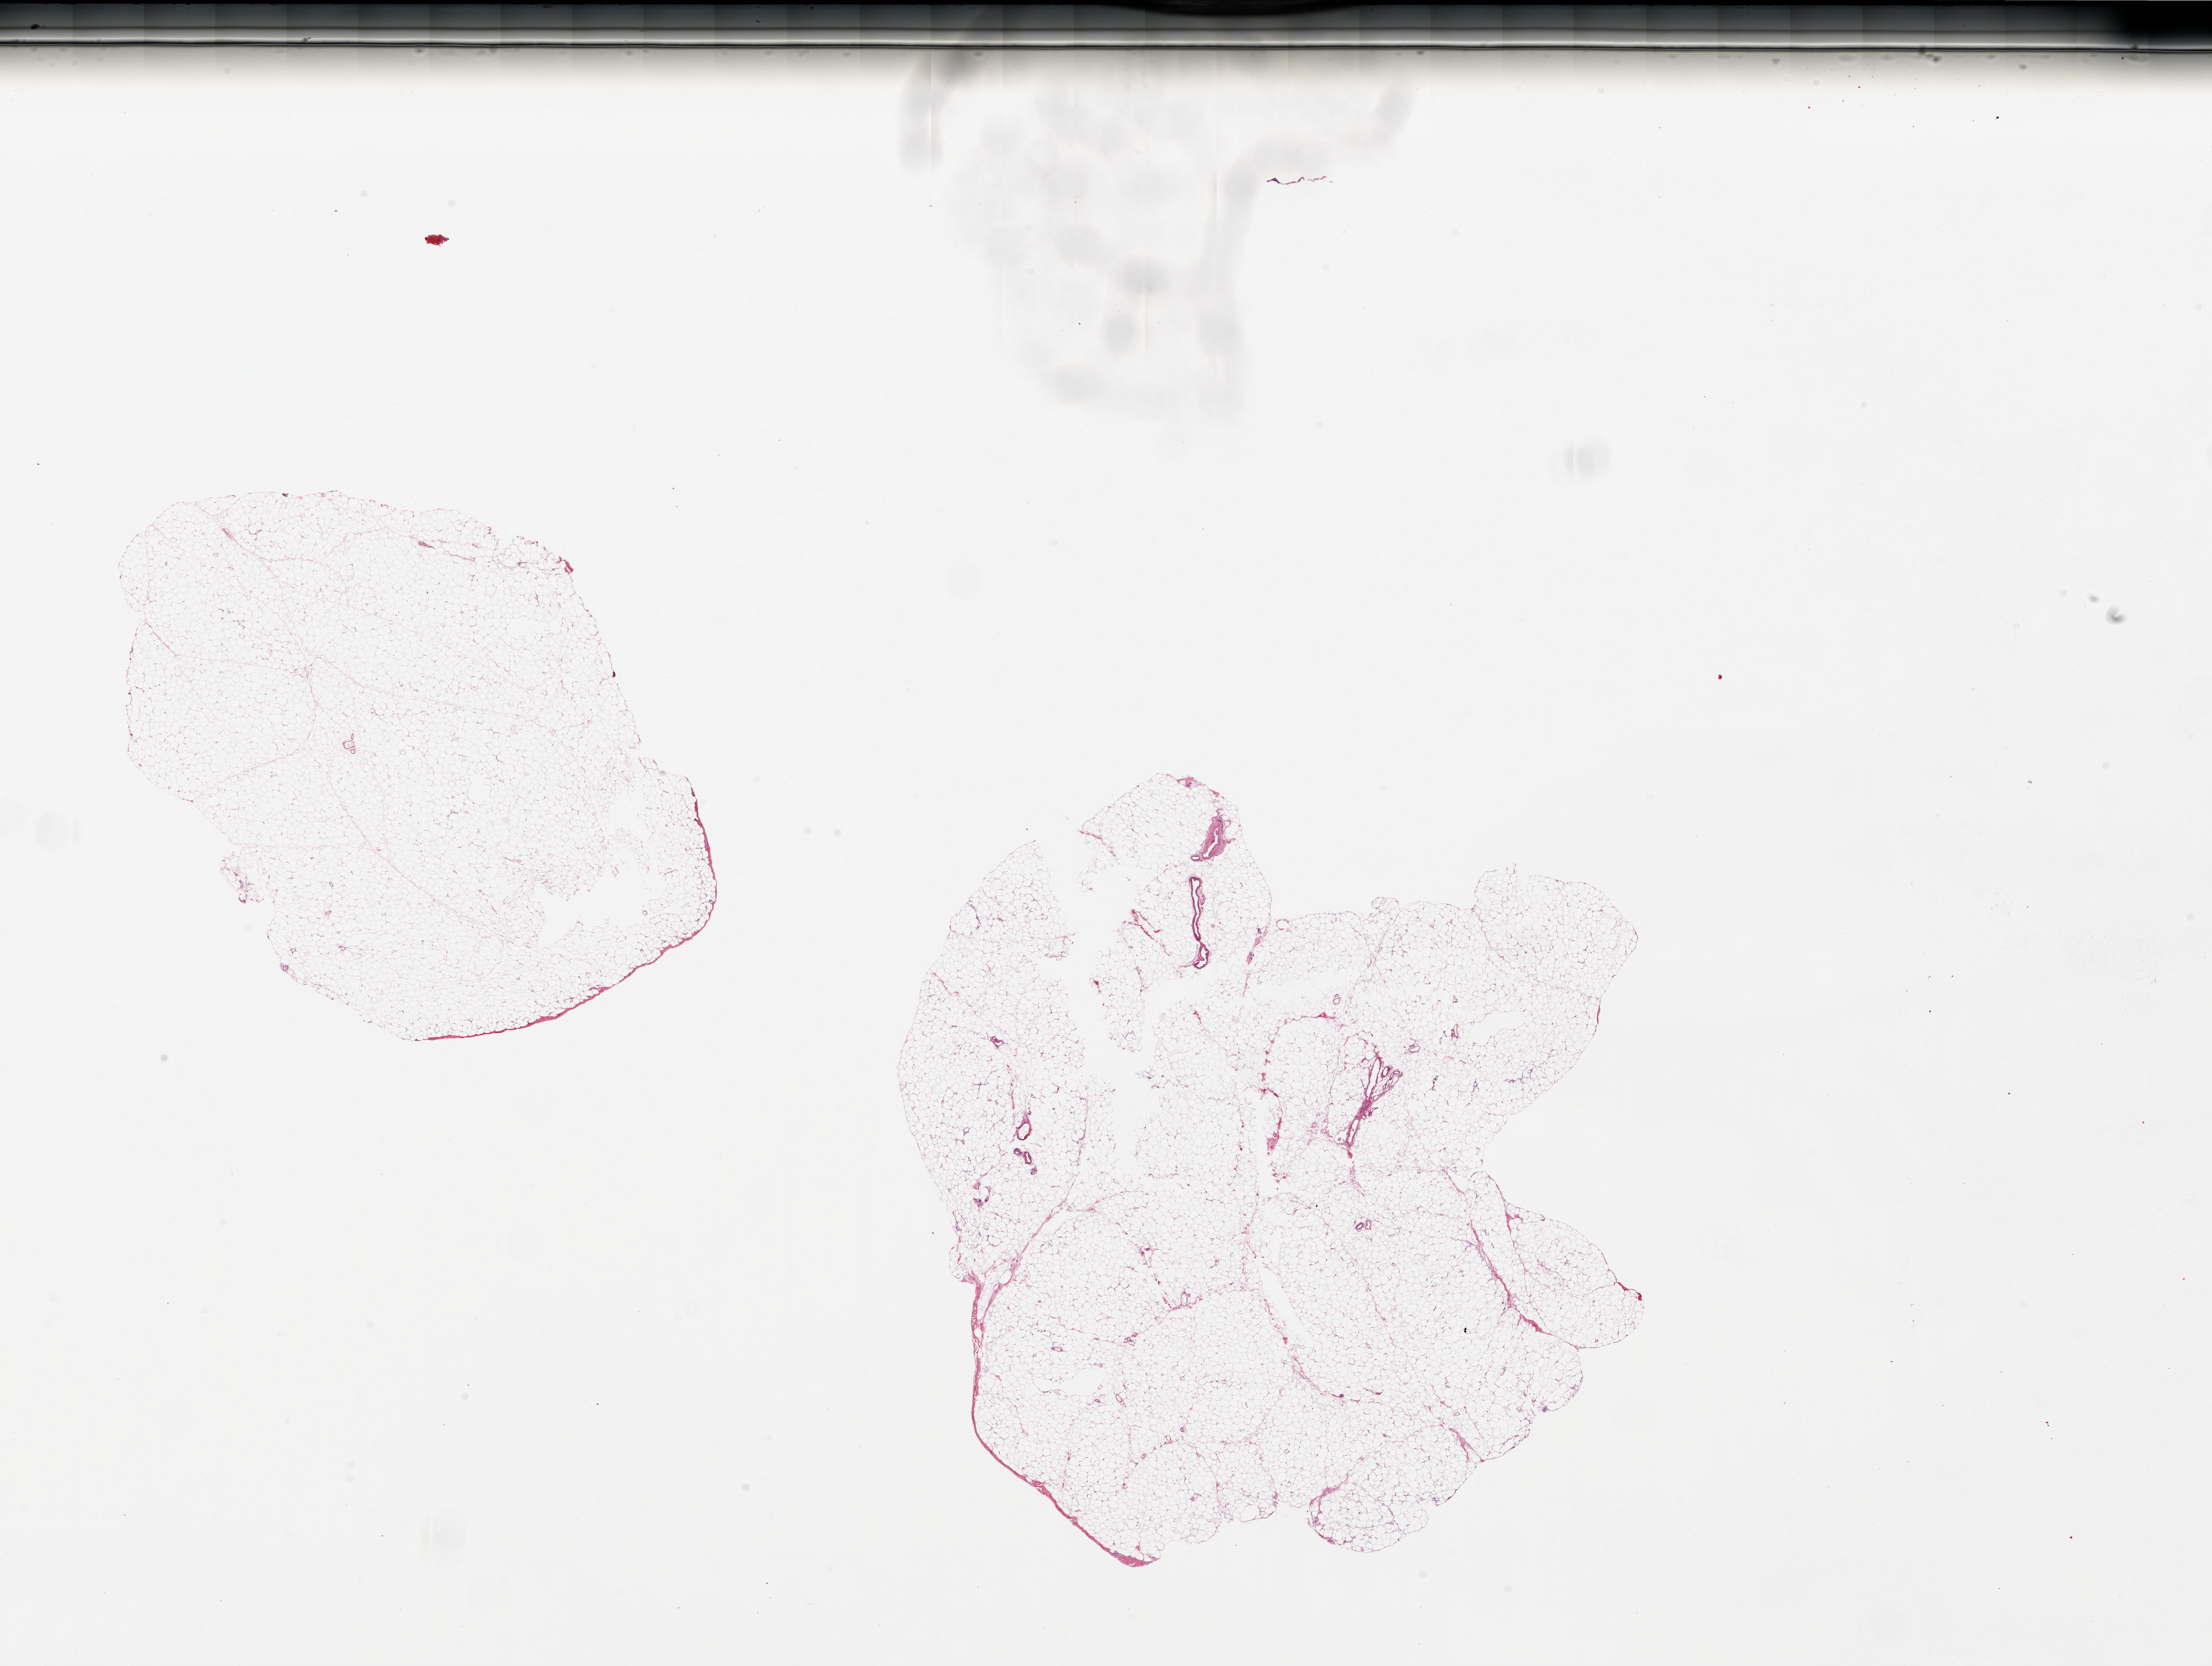
Whole-slide image, hematoxylin and eosin (H&E) stain — whole scanned area (about 30.5 x 23.0 mm, slide scanned at 20x) shown as a low-resolution overview. PAXgene-fixed, paraffin-embedded tissue. Target tissue: omentum. Donor tissue sample. Female donor.
Reviewer comment on this tissue sample: 2 pieces, 9x7 & 11.5x11mm.